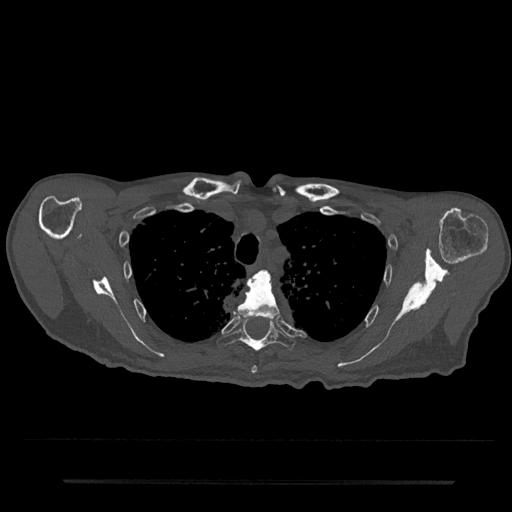
CT including the spine, one axial slice. Position 598 of 797 along the scan axis. Bone window (W 1800 / L 400 HU). 512 × 512 image matrix. Patient: male, 74 years. Case-level facts recorded for this patient, not image findings: primary cancer: prostate.
Annotated regions visible in this slice (semi-automatic segmentation, software-assisted and operator-edited):
- T4 vertebra: bounding box <237,271,280,374> (left, top, right, bottom; pixels)
- T5 vertebra: <217,315,295,352>